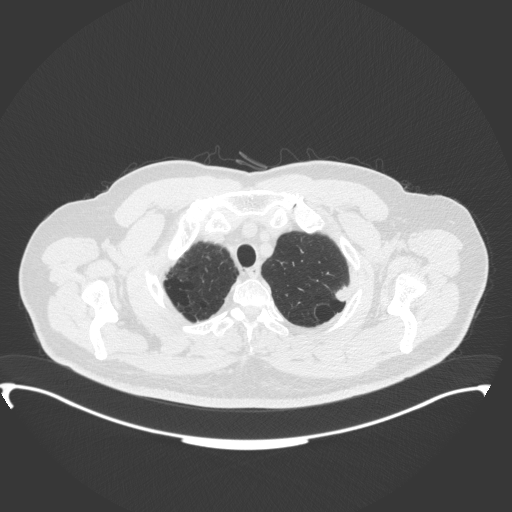
Chest CT, one axial slice. Position 326 of 350 along the scan axis. 120 kVp. Lung window (W 1500 / L -600 HU). 1 mm slice thickness. 512 × 512 image matrix. Patient: male, 64 years. Case-level facts recorded for this patient, not image findings: clinical TNM (as recorded): T1c N1 M1.
Structures marked on this image (rectangle marked by the reading radiologist):
- lung tumour (recorded histology: adenocarcinoma): box from (x=330, y=284) to (x=351, y=308) px